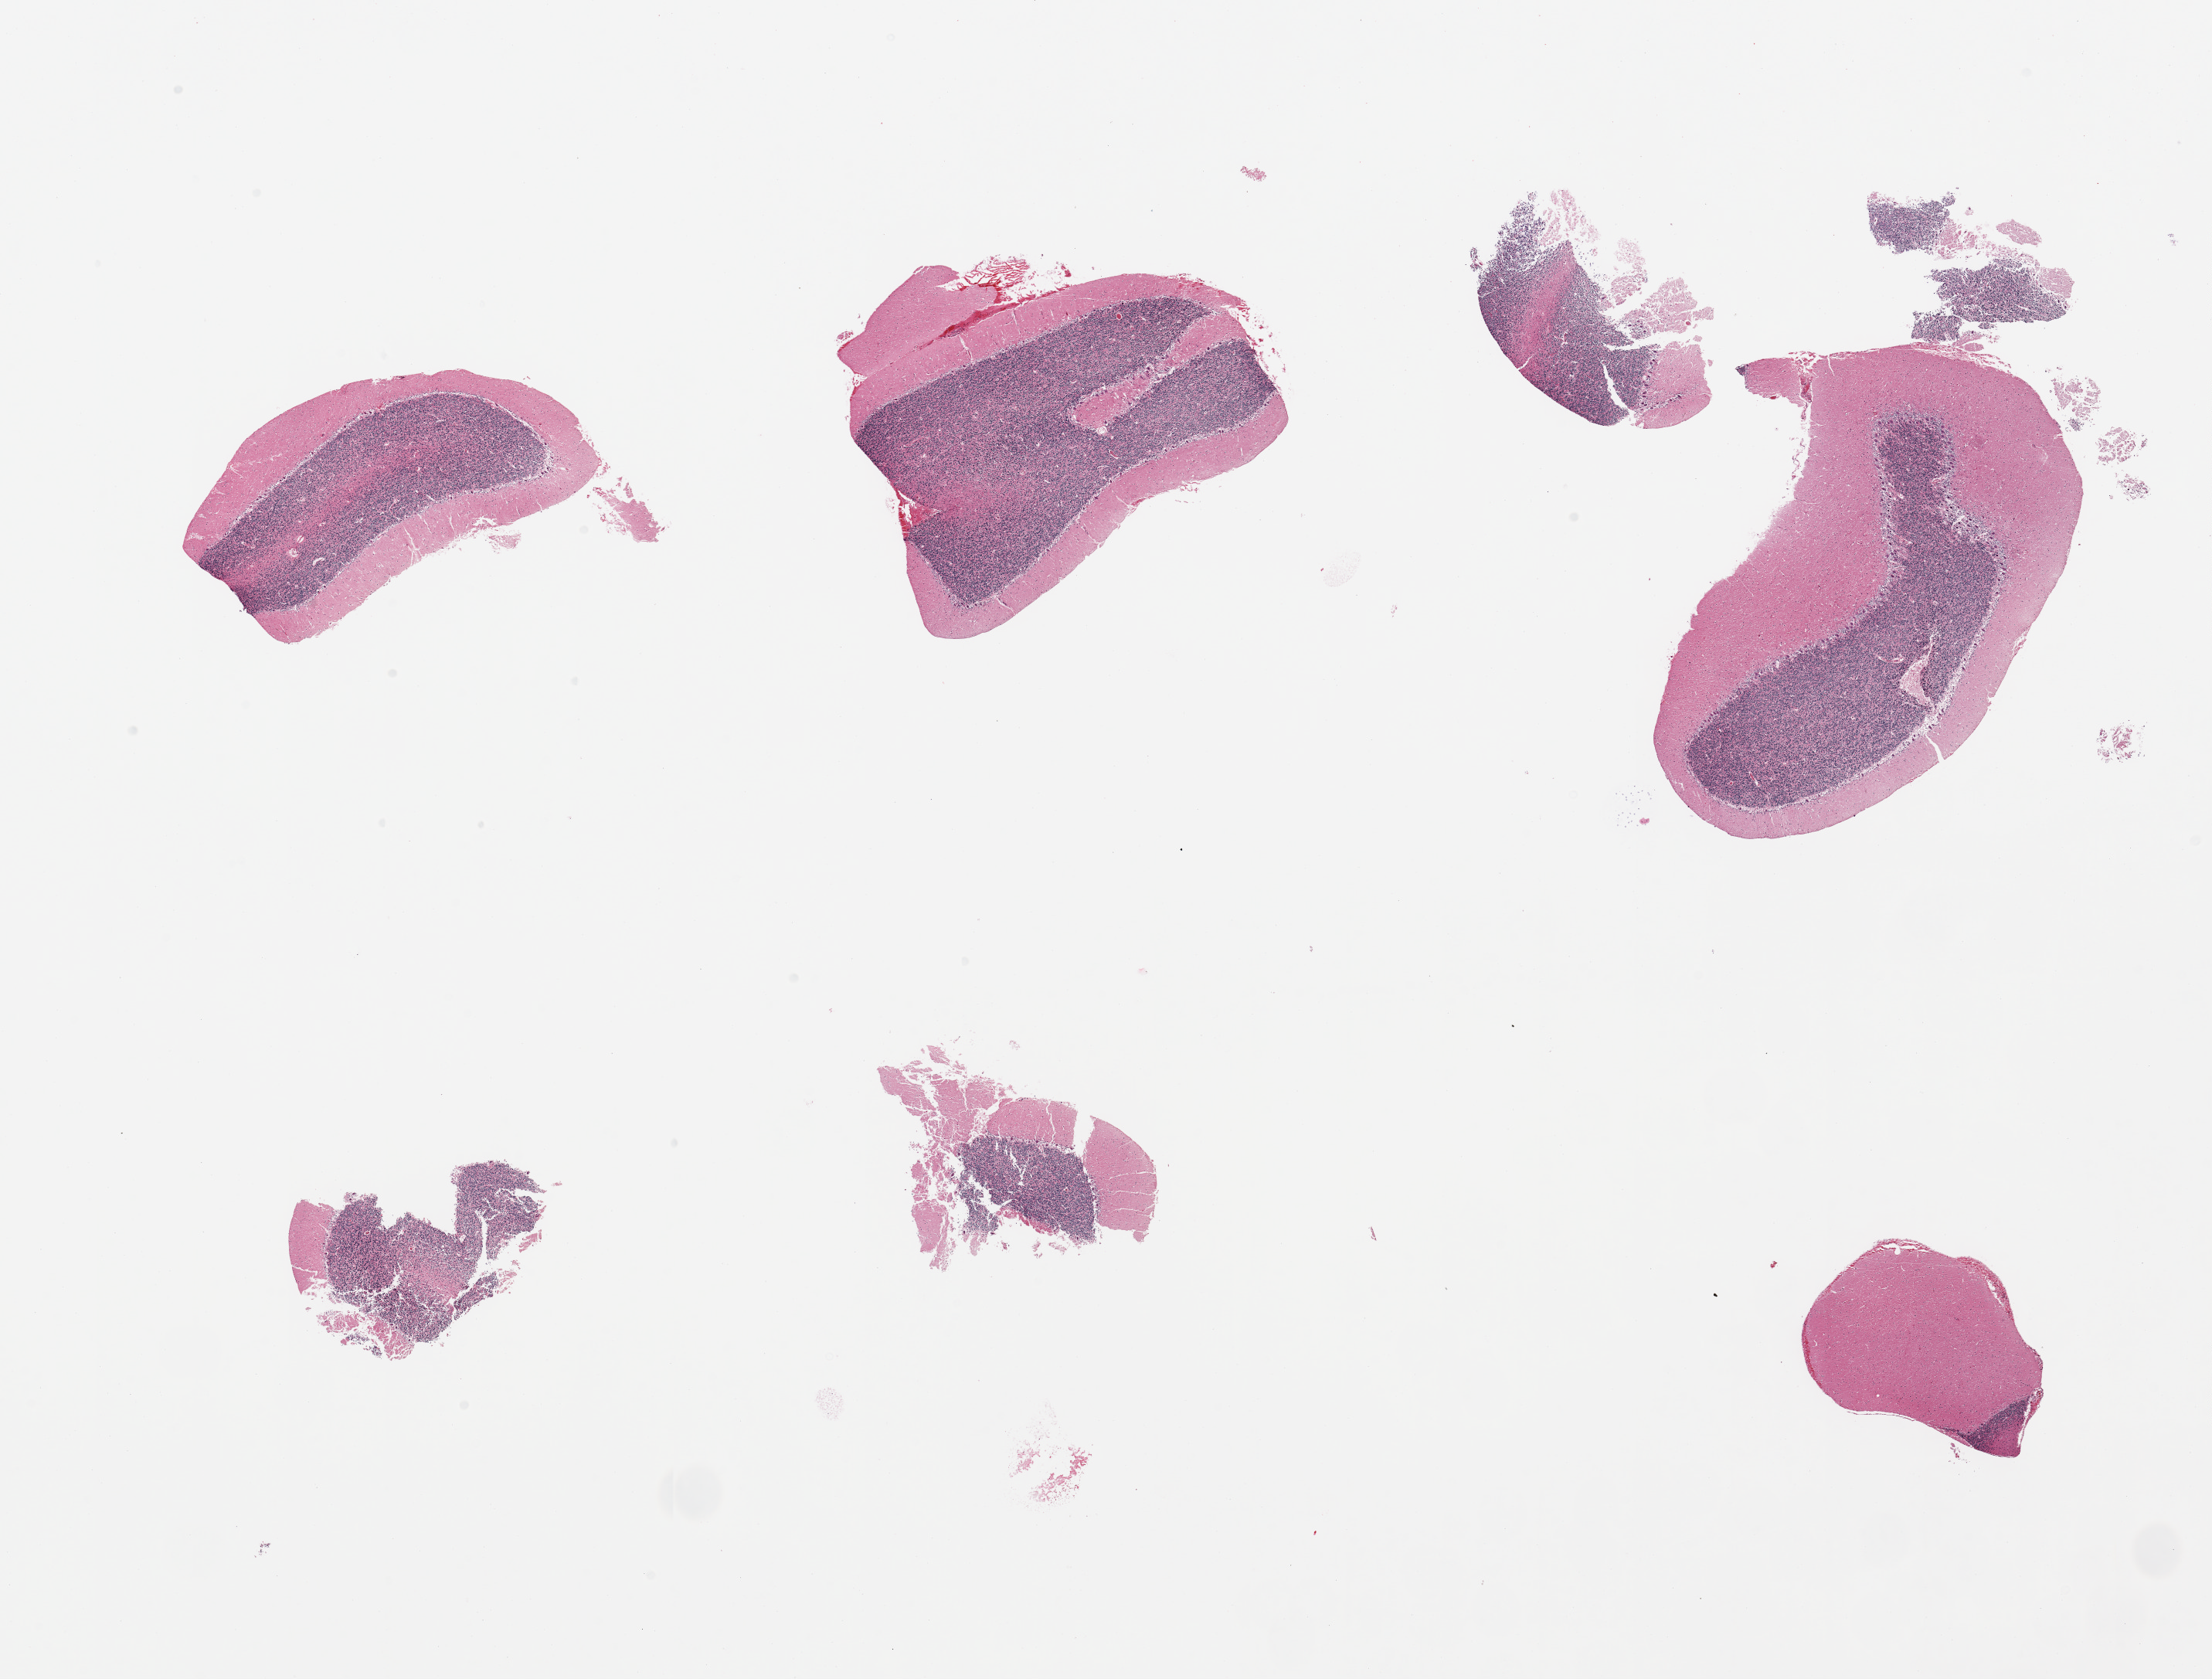
Hematoxylin and eosin (H&E) whole-slide image — a low-resolution overview of the entire scanned area, about 22.6 x 17.2 mm (slide scanned at 20x); PAXgene-fixed, paraffin-embedded tissue; sampled site (target tissue): cerebellum; tissue donor sample. Male donor.
Review note (as recorded): 6 fragmented pieces.